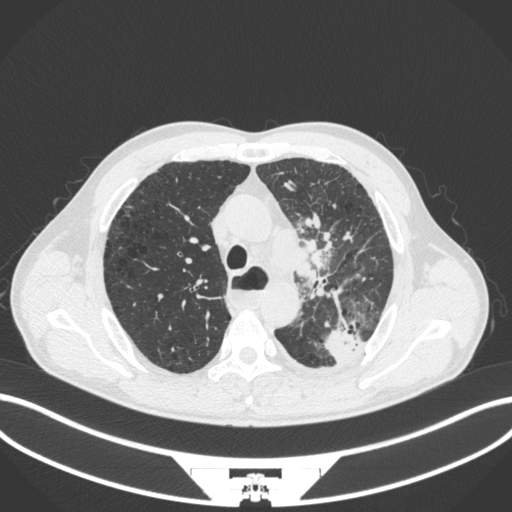
Chest CT, one axial slice; position 282 of 411 along the scan axis; reconstruction kernel B31f; lung window (W 1500 / L -600 HU); 512 × 512 image matrix, field of view 400 × 400 mm. Patient: male, 57 years. Case-level facts recorded for this patient, not image findings: clinical TNM (as recorded): T2a N1 M0.
Structures marked on this image (bounding box drawn by a radiologist):
- lung tumour (recorded histology: squamous cell carcinoma): box from (x=279, y=228) to (x=336, y=297) px